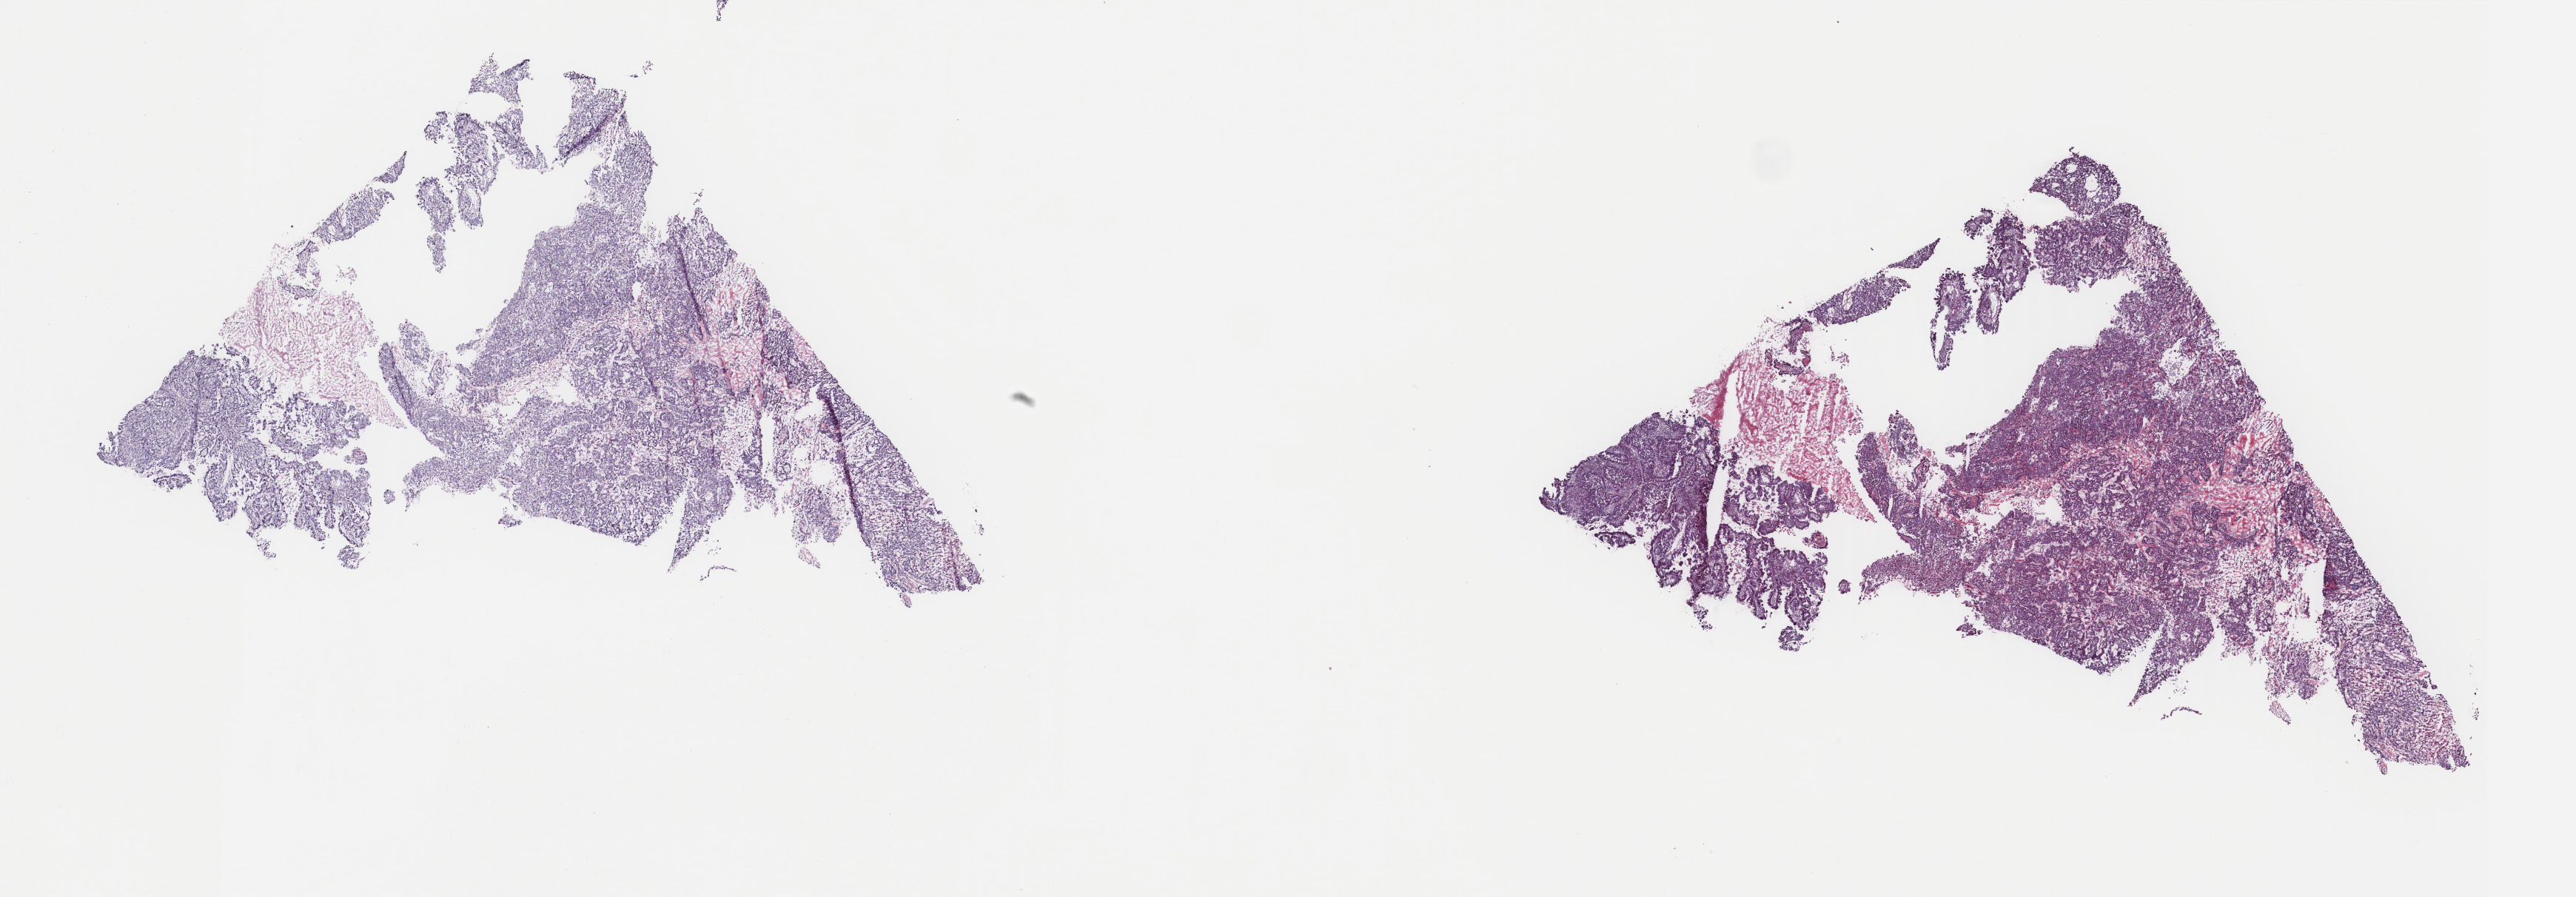
H&E-stained whole-slide image, low-resolution overview of the scanned area, about 27.6 x 9.6 mm (from a 40x scan). Frozen section. Primary tumour sample from the uterus. Female, age 68 years at initial diagnosis.
Histologic diagnosis: Serous cystadenocarcinoma, NOS (endometrium).